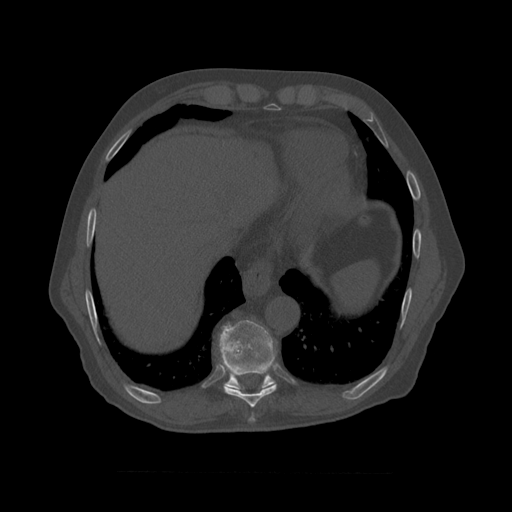
CT including the spine, one axial slice. Position 438 of 450 along the scan axis. Reconstruction kernel STANDARD. Bone window (W 1800 / L 400 HU). 1.25 mm slice thickness. 512 × 512 image matrix, field of view 405 × 405 mm. Patient age 75 years. Case-level facts recorded for this patient, not image findings: primary cancer: prostate.
Structures marked on this image (semi-automatic segmentation, software-assisted and operator-edited):
- T8 vertebra: bounding box [x1, y1, x2, y2] px = [219, 333, 277, 408]
- T9 vertebra: [220, 320, 276, 389]